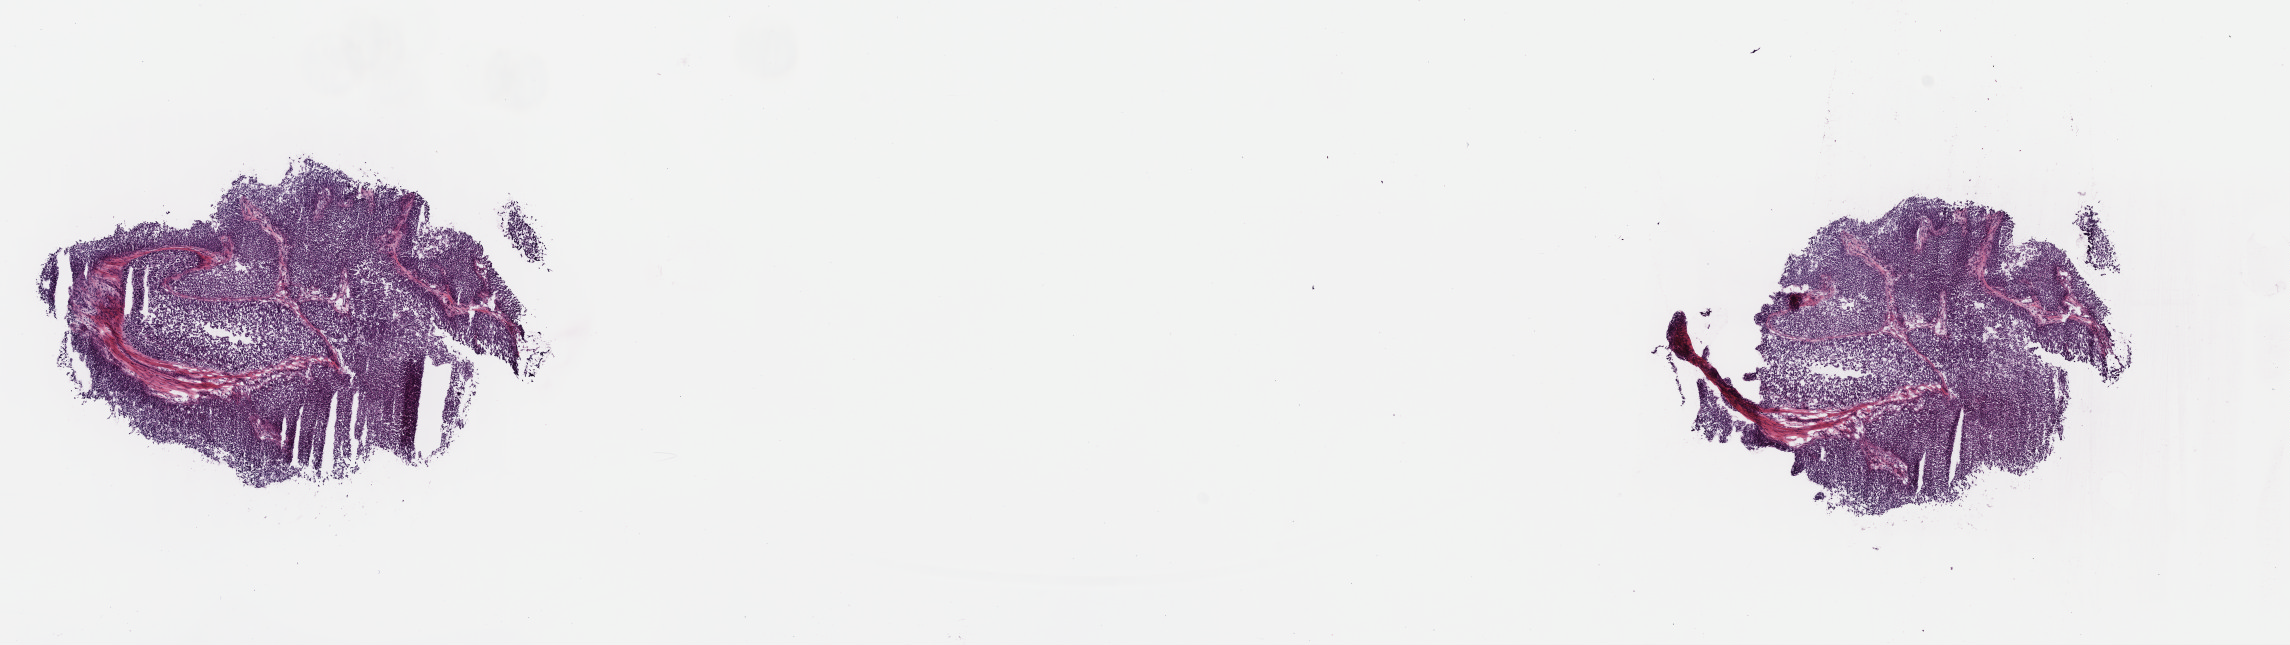
Whole-slide histology image, H&E, whole scanned area (about 18.0 x 5.1 mm) shown as a low-resolution overview. Frozen section from the top of the tissue portion. Bladder, primary tumour sample. Patient: female, age at initial diagnosis 58 years.
Histologic diagnosis: Papillary transitional cell carcinoma.